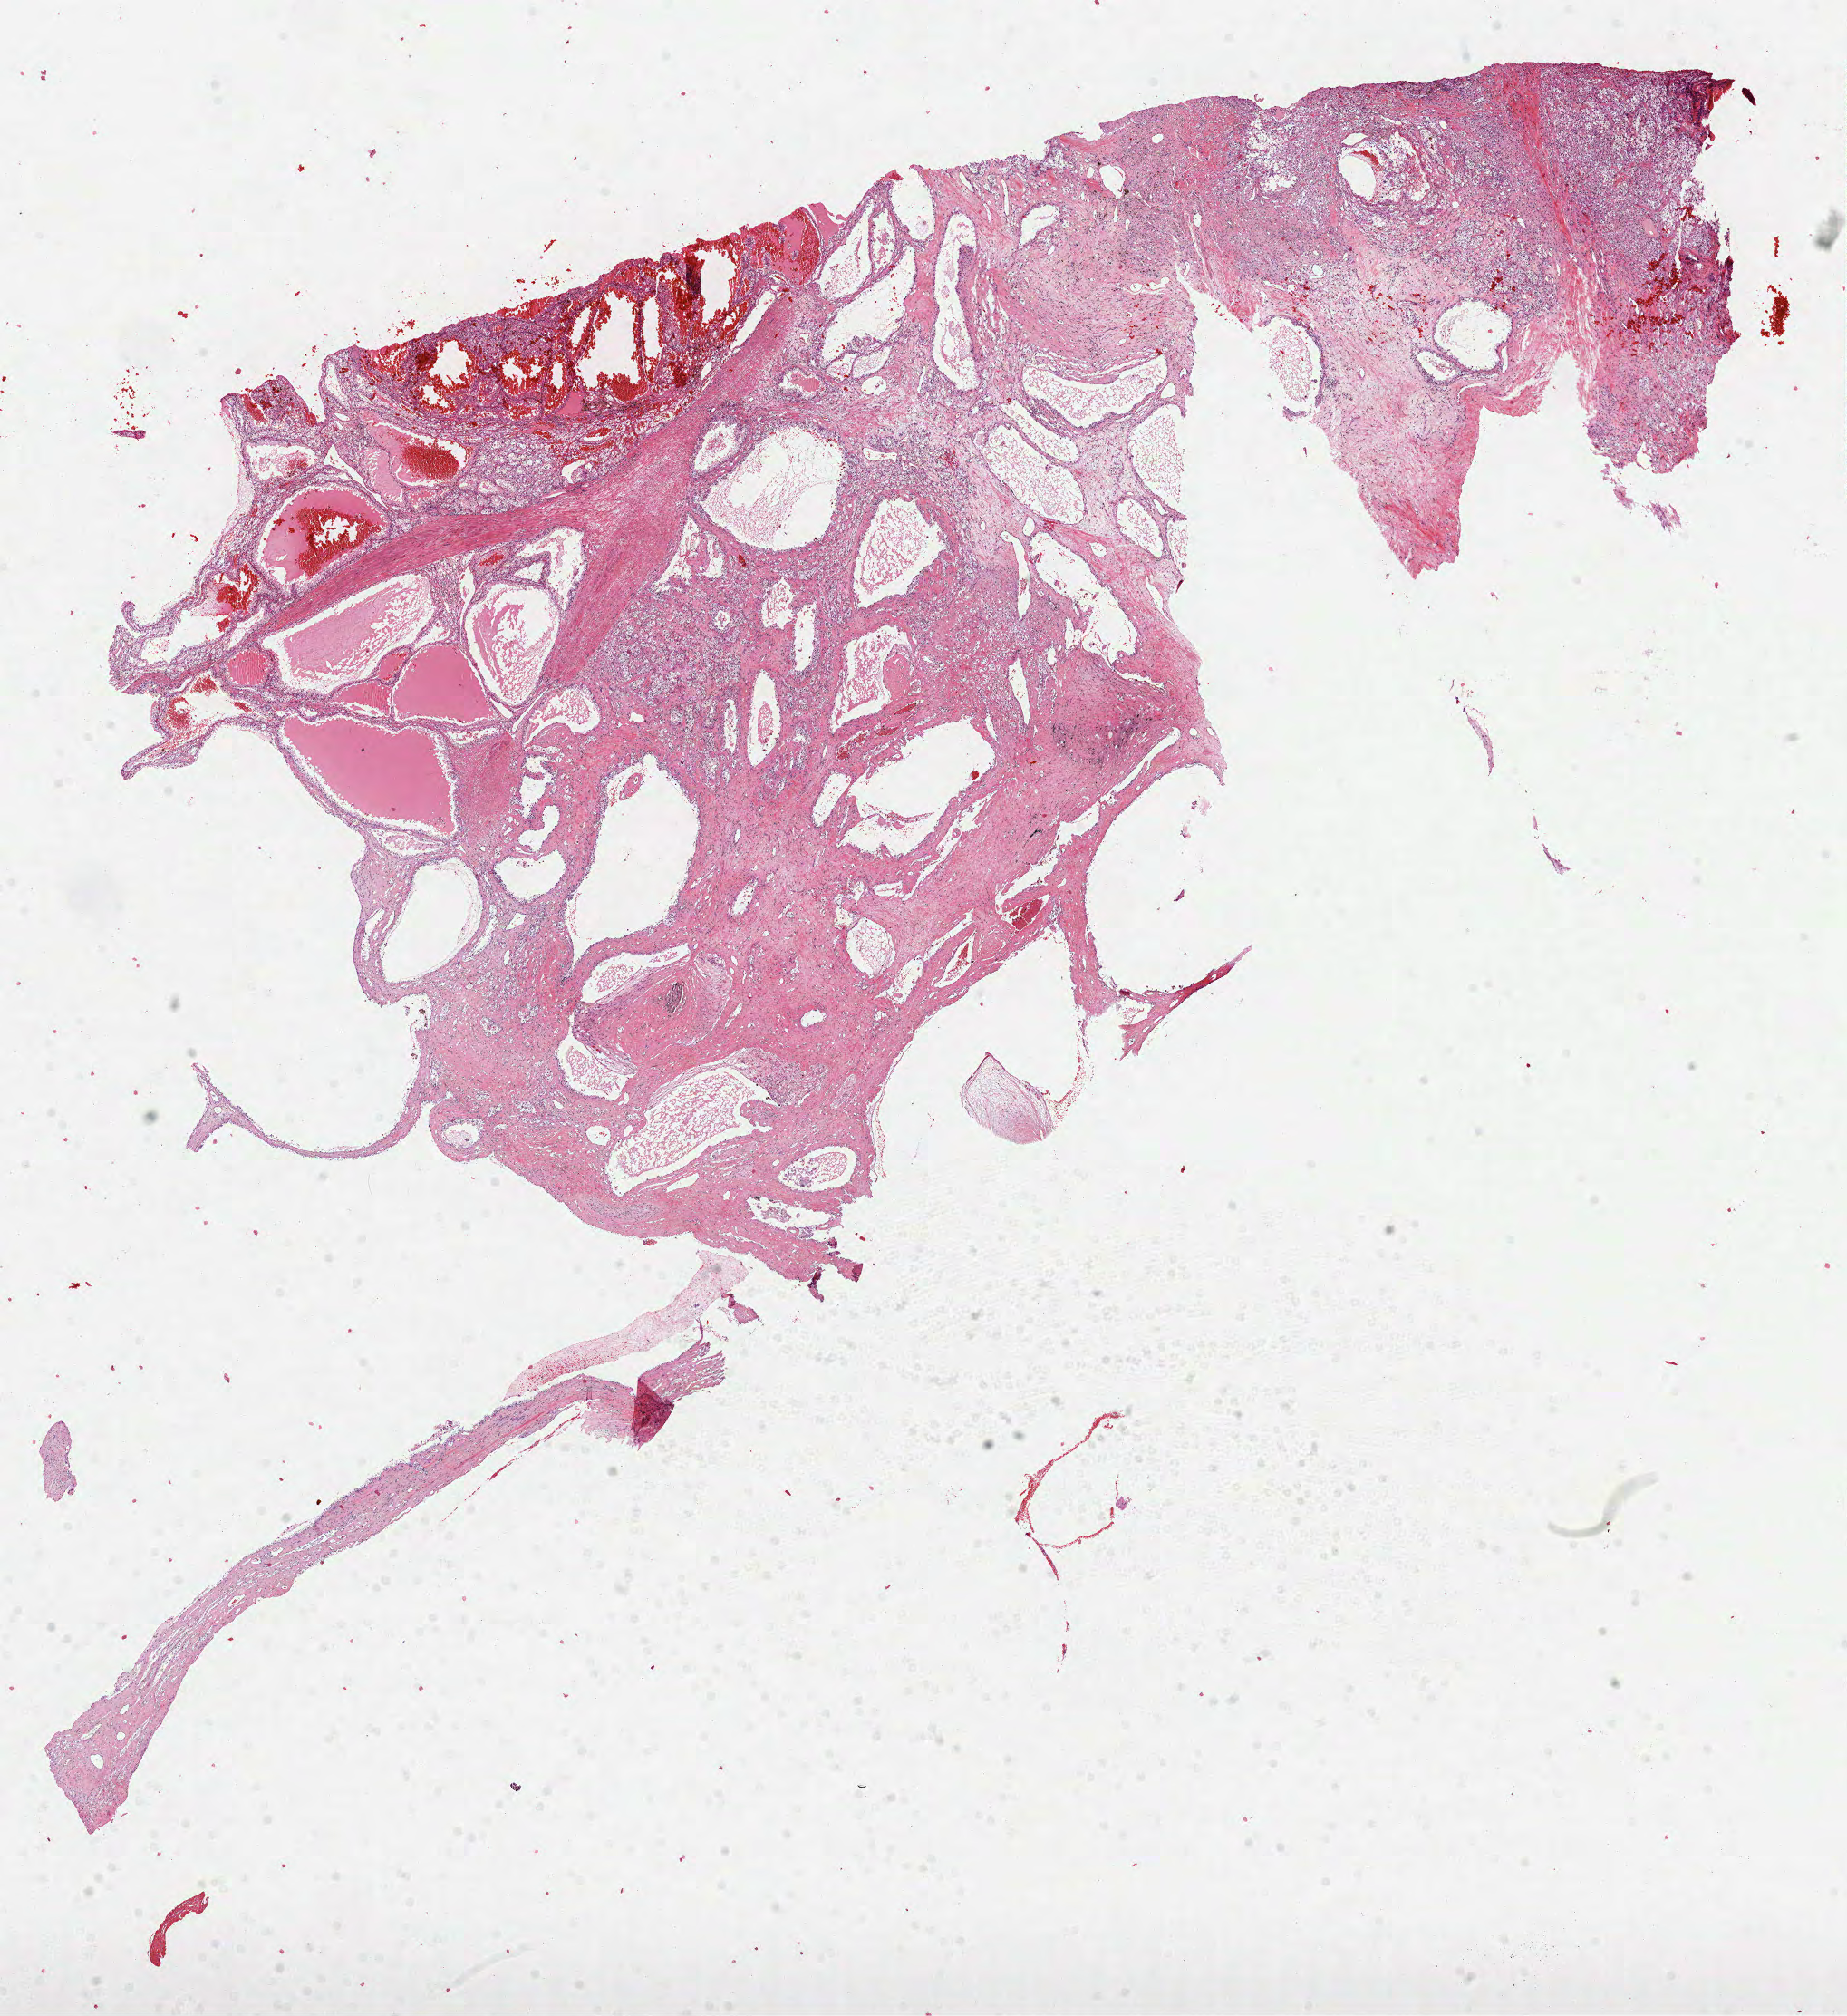
Digitized H&E-stained tissue section (whole slide), whole scanned area (about 16.4 x 17.9 mm) shown as a low-resolution overview. Formalin-fixed paraffin-embedded (FFPE) diagnostic section. Primary tumour sample from the kidney. Patient: male, age at initial diagnosis 63 years.
Histologic diagnosis: Clear cell adenocarcinoma, NOS.